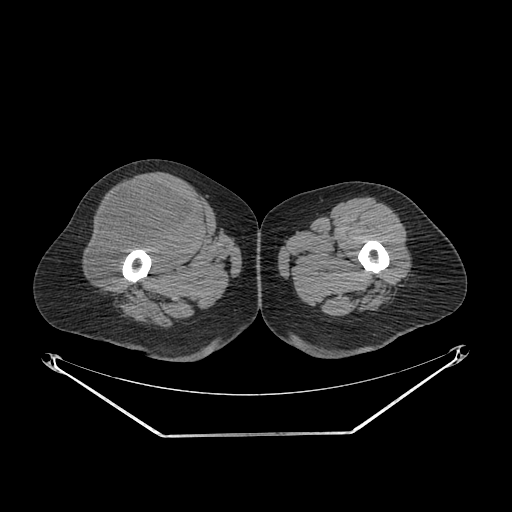
CT of an extremity soft-tissue mass (from a PET/CT study), one axial slice. Position 258 of 311 along the scan axis. 140 kVp. Soft-tissue window (W 400 / L 40 HU). 3.75 mm slice thickness. 512 × 512 image matrix. Female patient. From the clinical record (not read from this slice): histological type: pleiomorphic undifferentiated sarcoma; grade: high; site of the primary tumour: right quadricep.
Structures marked on this image (expert contour drawn on MRI and transferred to this co-registered scan by the dataset authors):
- tumour plus oedema (research contour): bounding box <91,183,197,286> (left, top, right, bottom; pixels)
- tumour (research contour): <91,183,197,286>